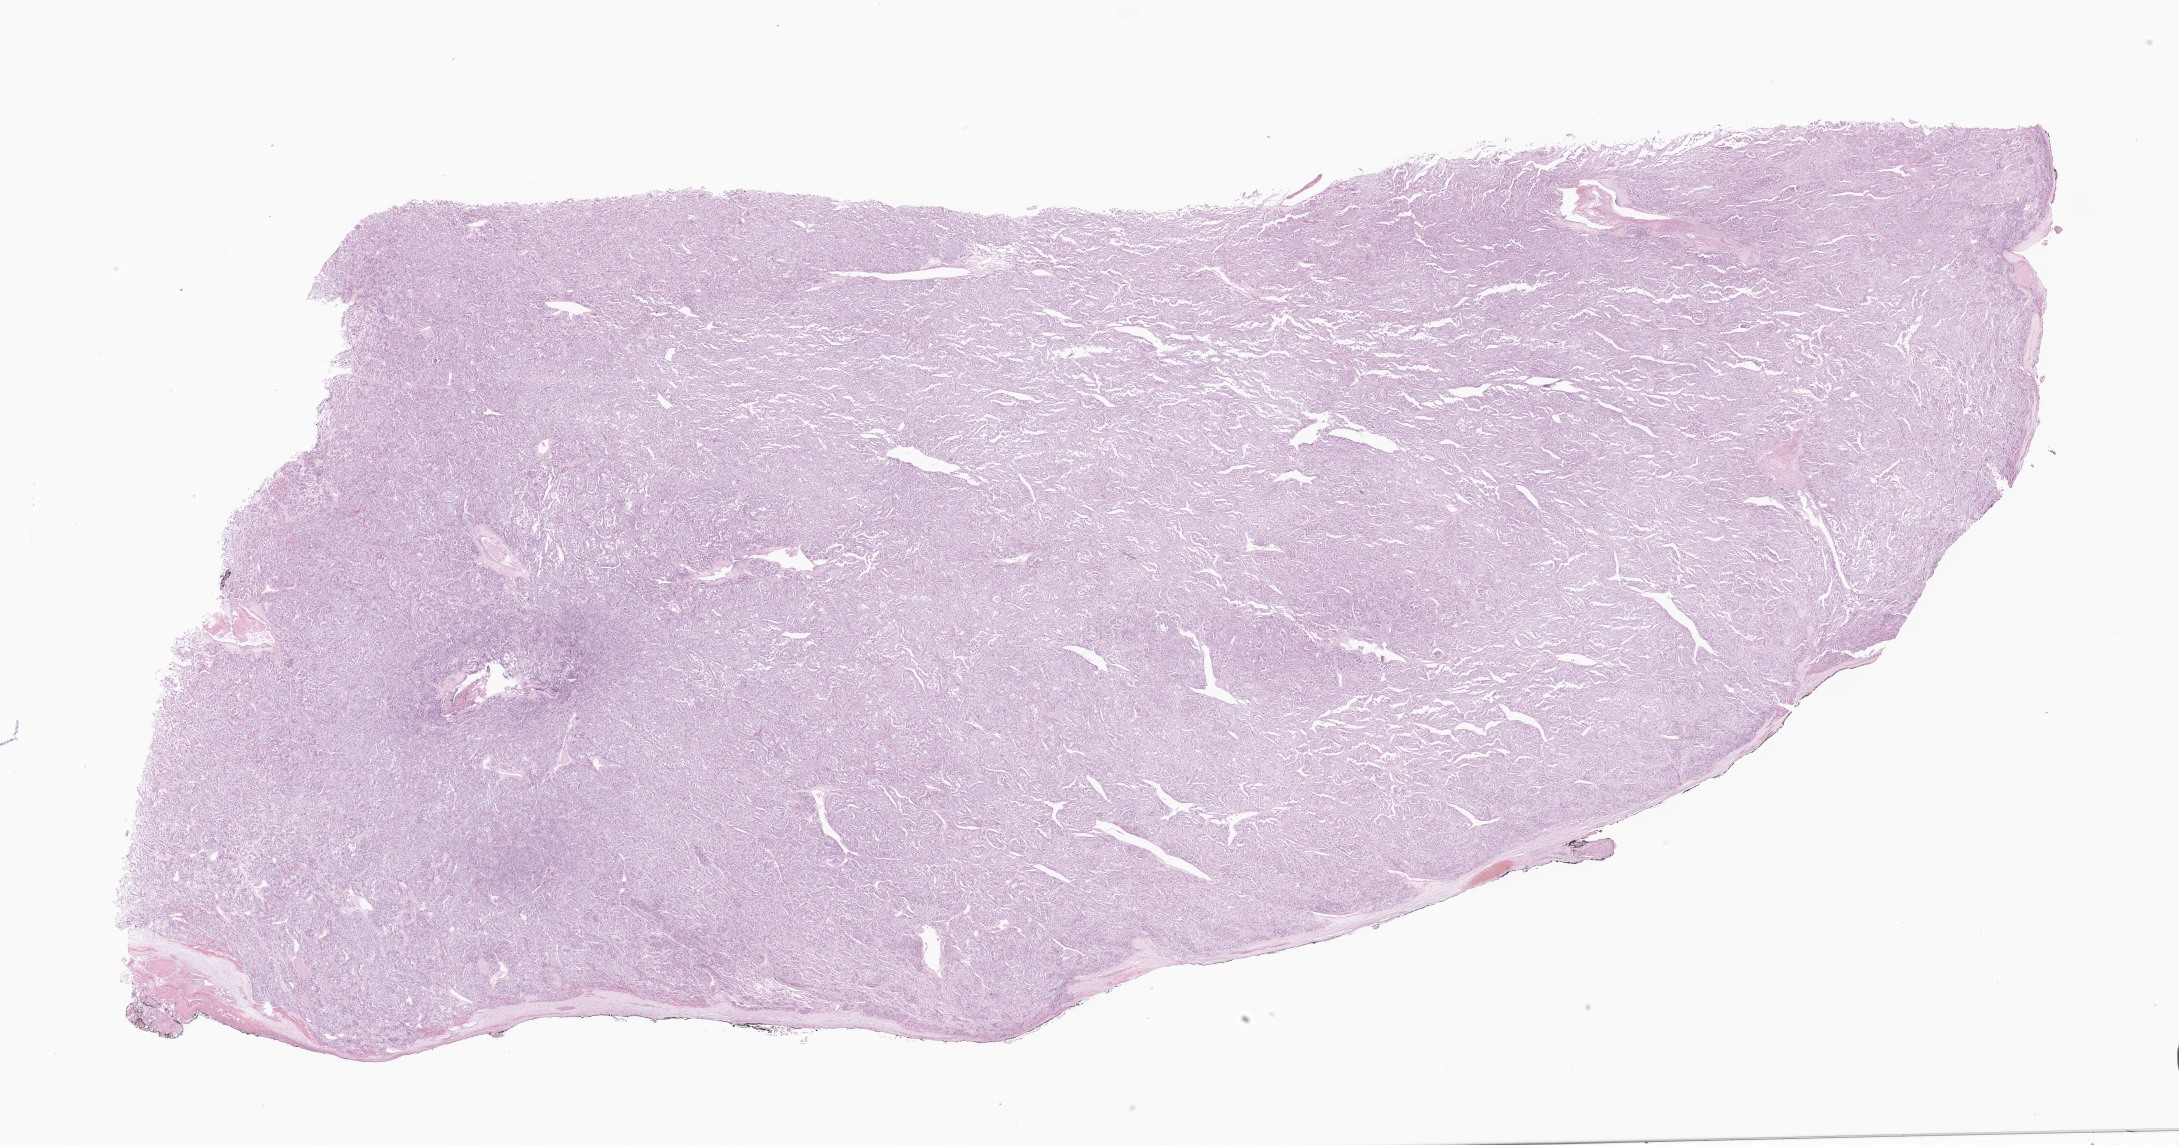
Digitized H&E-stained section of tumor tissue from the retroperitoneum, a low-resolution overview of the entire scanned area, about 36.8 x 19.3 mm. Patient male; age 138 months.
Specimen: formalin-fixed, paraffin-embedded (FFPE) tissue.